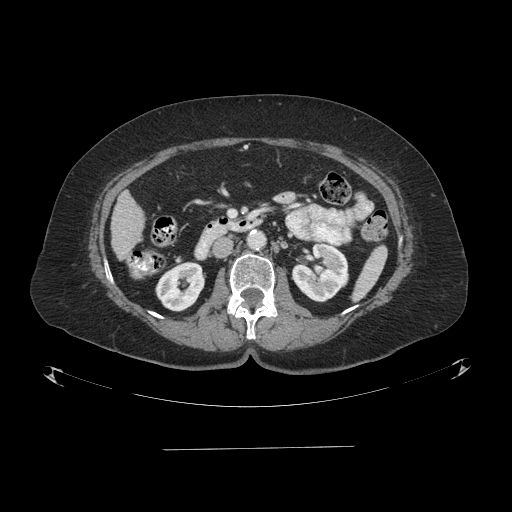
Contrast-enhanced abdominal CT (liver protocol), one axial slice. Slice 24 of 103 in the series (ordered by position). One of 2 acquisitions stored at this slice position. Soft-tissue window (W 400 / L 40 HU). 2.5 mm slice thickness. 512 × 512 image matrix. Case-level facts recorded for this patient, not image findings: diagnosis: hepatocellular carcinoma (patient treated with transarterial chemoembolisation; whether this scan precedes or follows treatment is not stated here); TNM stage (as recorded): Stage-IIIA; Child-Pugh class: A; tumour nodularity: multinodular; tumour size: 5.2 cm.
Structures marked on this image (semi-automatically segmented with operator editing):
- liver parenchyma outside the tumour (the mass and vessels are separate outlines, so this box may not span the whole liver): box from (x=110, y=190) to (x=144, y=260) px